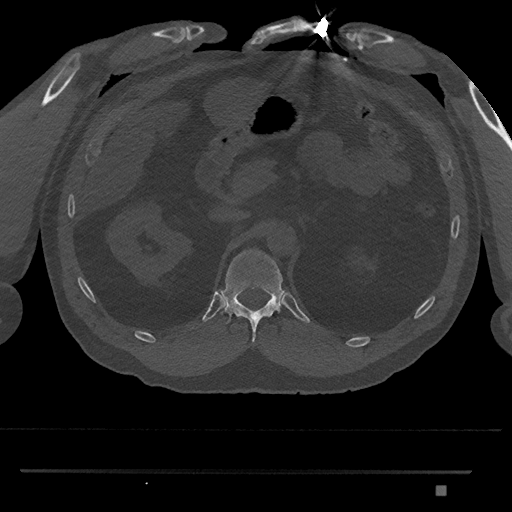
CT including the spine, one axial slice; position 885 of 1134 along the scan axis; reconstruction kernel Br40s/3; 120 kVp; bone window (W 1800 / L 400 HU); 0.5 mm slice thickness; 512 × 512 image matrix. Male patient, age 65 years. Case-level facts recorded for this patient, not image findings: primary cancer: prostate.
Annotated regions visible in this slice (semi-automatically segmented with operator editing):
- T12 vertebra: bounding box <219,249,285,344> (left, top, right, bottom; pixels)